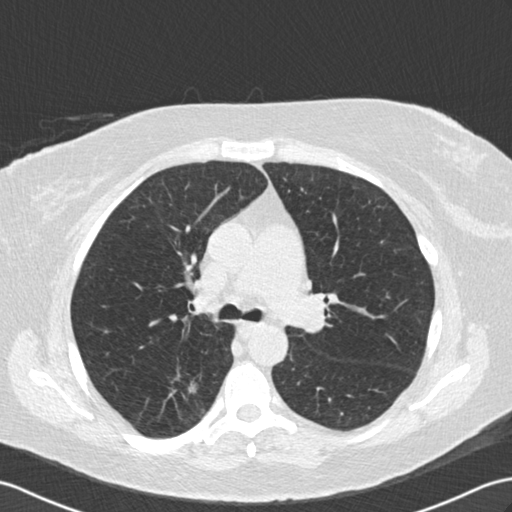
Chest CT (low-dose screening protocol), one axial image; second annual screen; lung window (W 1500 / L -600 HU); standard (soft-tissue) reconstruction kernel (B30f); slice 55 of 154 in the series; 512 × 512 image matrix, field of view 352 × 352 mm. Female, age 65 years at enrolment.
Lesion marked by an expert reader, bounding box (x1, y1, x2, y2) in pixels: (156, 357, 217, 417). Reader record for this screening exam (exam-level; its link to the box is not recorded): non-calcified nodule or mass ≥4 mm, right lower lobe, 18 × 16 mm, spiculated (stellate) margins, soft tissue attenuation, pre-existing on the prior screen: yes; interval growth: yes. Lung cancer was diagnosed 239 days after this screen: adenocarcinoma, NOS, right lower lobe, moderately differentiated (G2), stage IA (AJCC 6th edition), 25 mm at pathology.